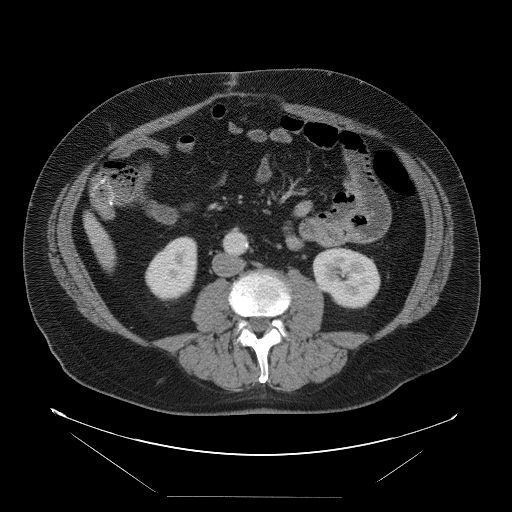
Contrast-enhanced abdominal CT, one axial slice. Position 14 of 114 along the scan axis. Intravenous contrast given. Soft-tissue window (W 400 / L 40 HU). 5 mm slice thickness. 512 × 512 image matrix, field of view 500 × 500 mm. Male patient, age 61 years. From the clinical record (not read from this slice): diagnosis: colorectal cancer liver metastases, imaged before liver resection; multiple liver metastases: no; largest metastasis: 6.5 cm; disease in both lobes: yes.
Annotated regions visible in this slice (expert manual segmentation):
- liver: bounding box (x1, y1, x2, y2) in pixels: (86, 216, 115, 268)